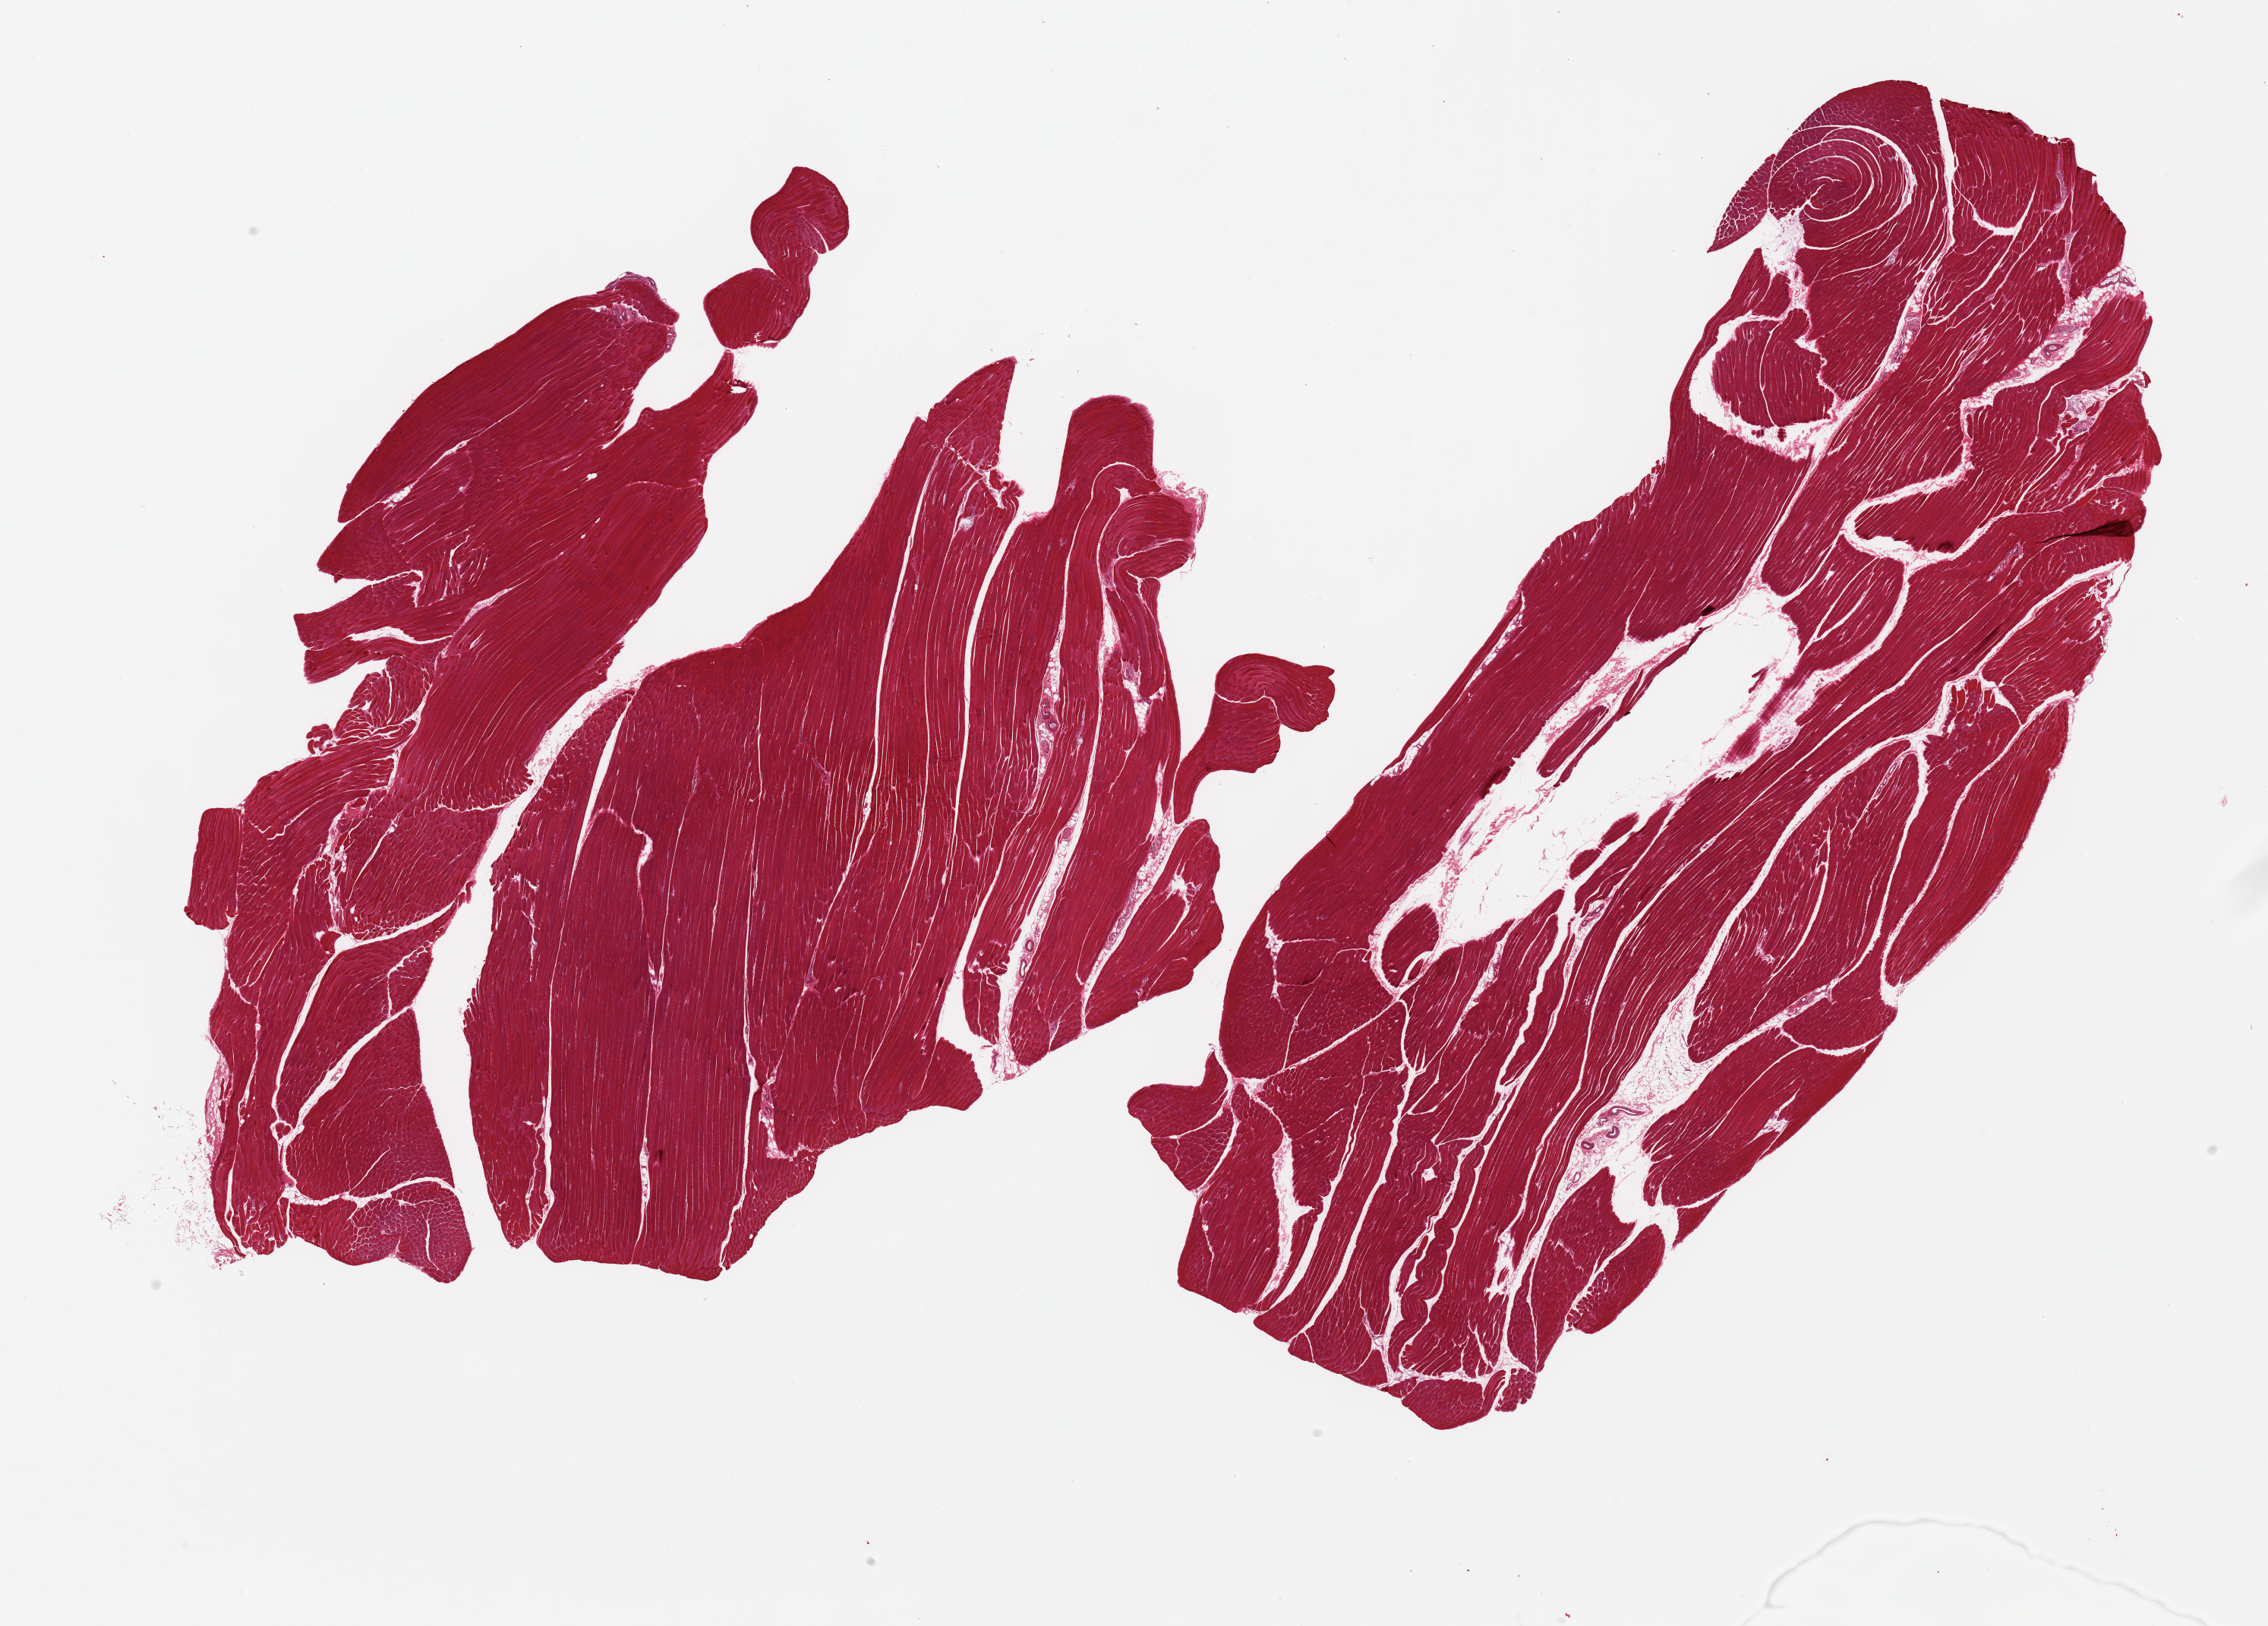
H&E whole-slide image, shown as a low-resolution overview of the whole scanned area (about 23.6 x 16.9 mm). PAXgene-fixed, paraffin-embedded tissue. Section of skeletal muscle (target tissue). Donor tissue sample. Donor sex: female.
• pathologist's review note for this sample: 2 pieces, ~5-10% interstitial fat